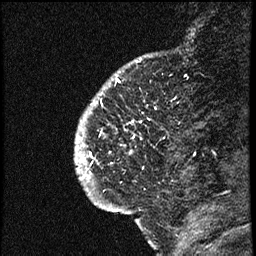
Breast MRI (dynamic contrast-enhanced), one sagittal slice; dynamic contrast-enhanced study with each time point stored as its own series, time point 2 of 3 at this slice position (early post-contrast, ordered by acquisition time); 1.5 T; TE 4.2 ms, TR 17.6 ms; 256 × 256 image matrix, field of view 200 × 200 mm. Female patient. From the clinical record (not read from this slice): setting: breast cancer imaged before/during neoadjuvant chemotherapy; receptor status: HER2-positive.
Outlined on this slice (semi-automatic segmentation, software-assisted and operator-edited):
- analysis volume of interest (the breast-tissue region the enhancement analysis was run in; not a lesion): bounding box <77,69,174,209> (left, top, right, bottom; pixels)
- tumour enhancement mask (voxels above the 100 % enhancement threshold inside the analysis volume of interest): <80,80,119,180>